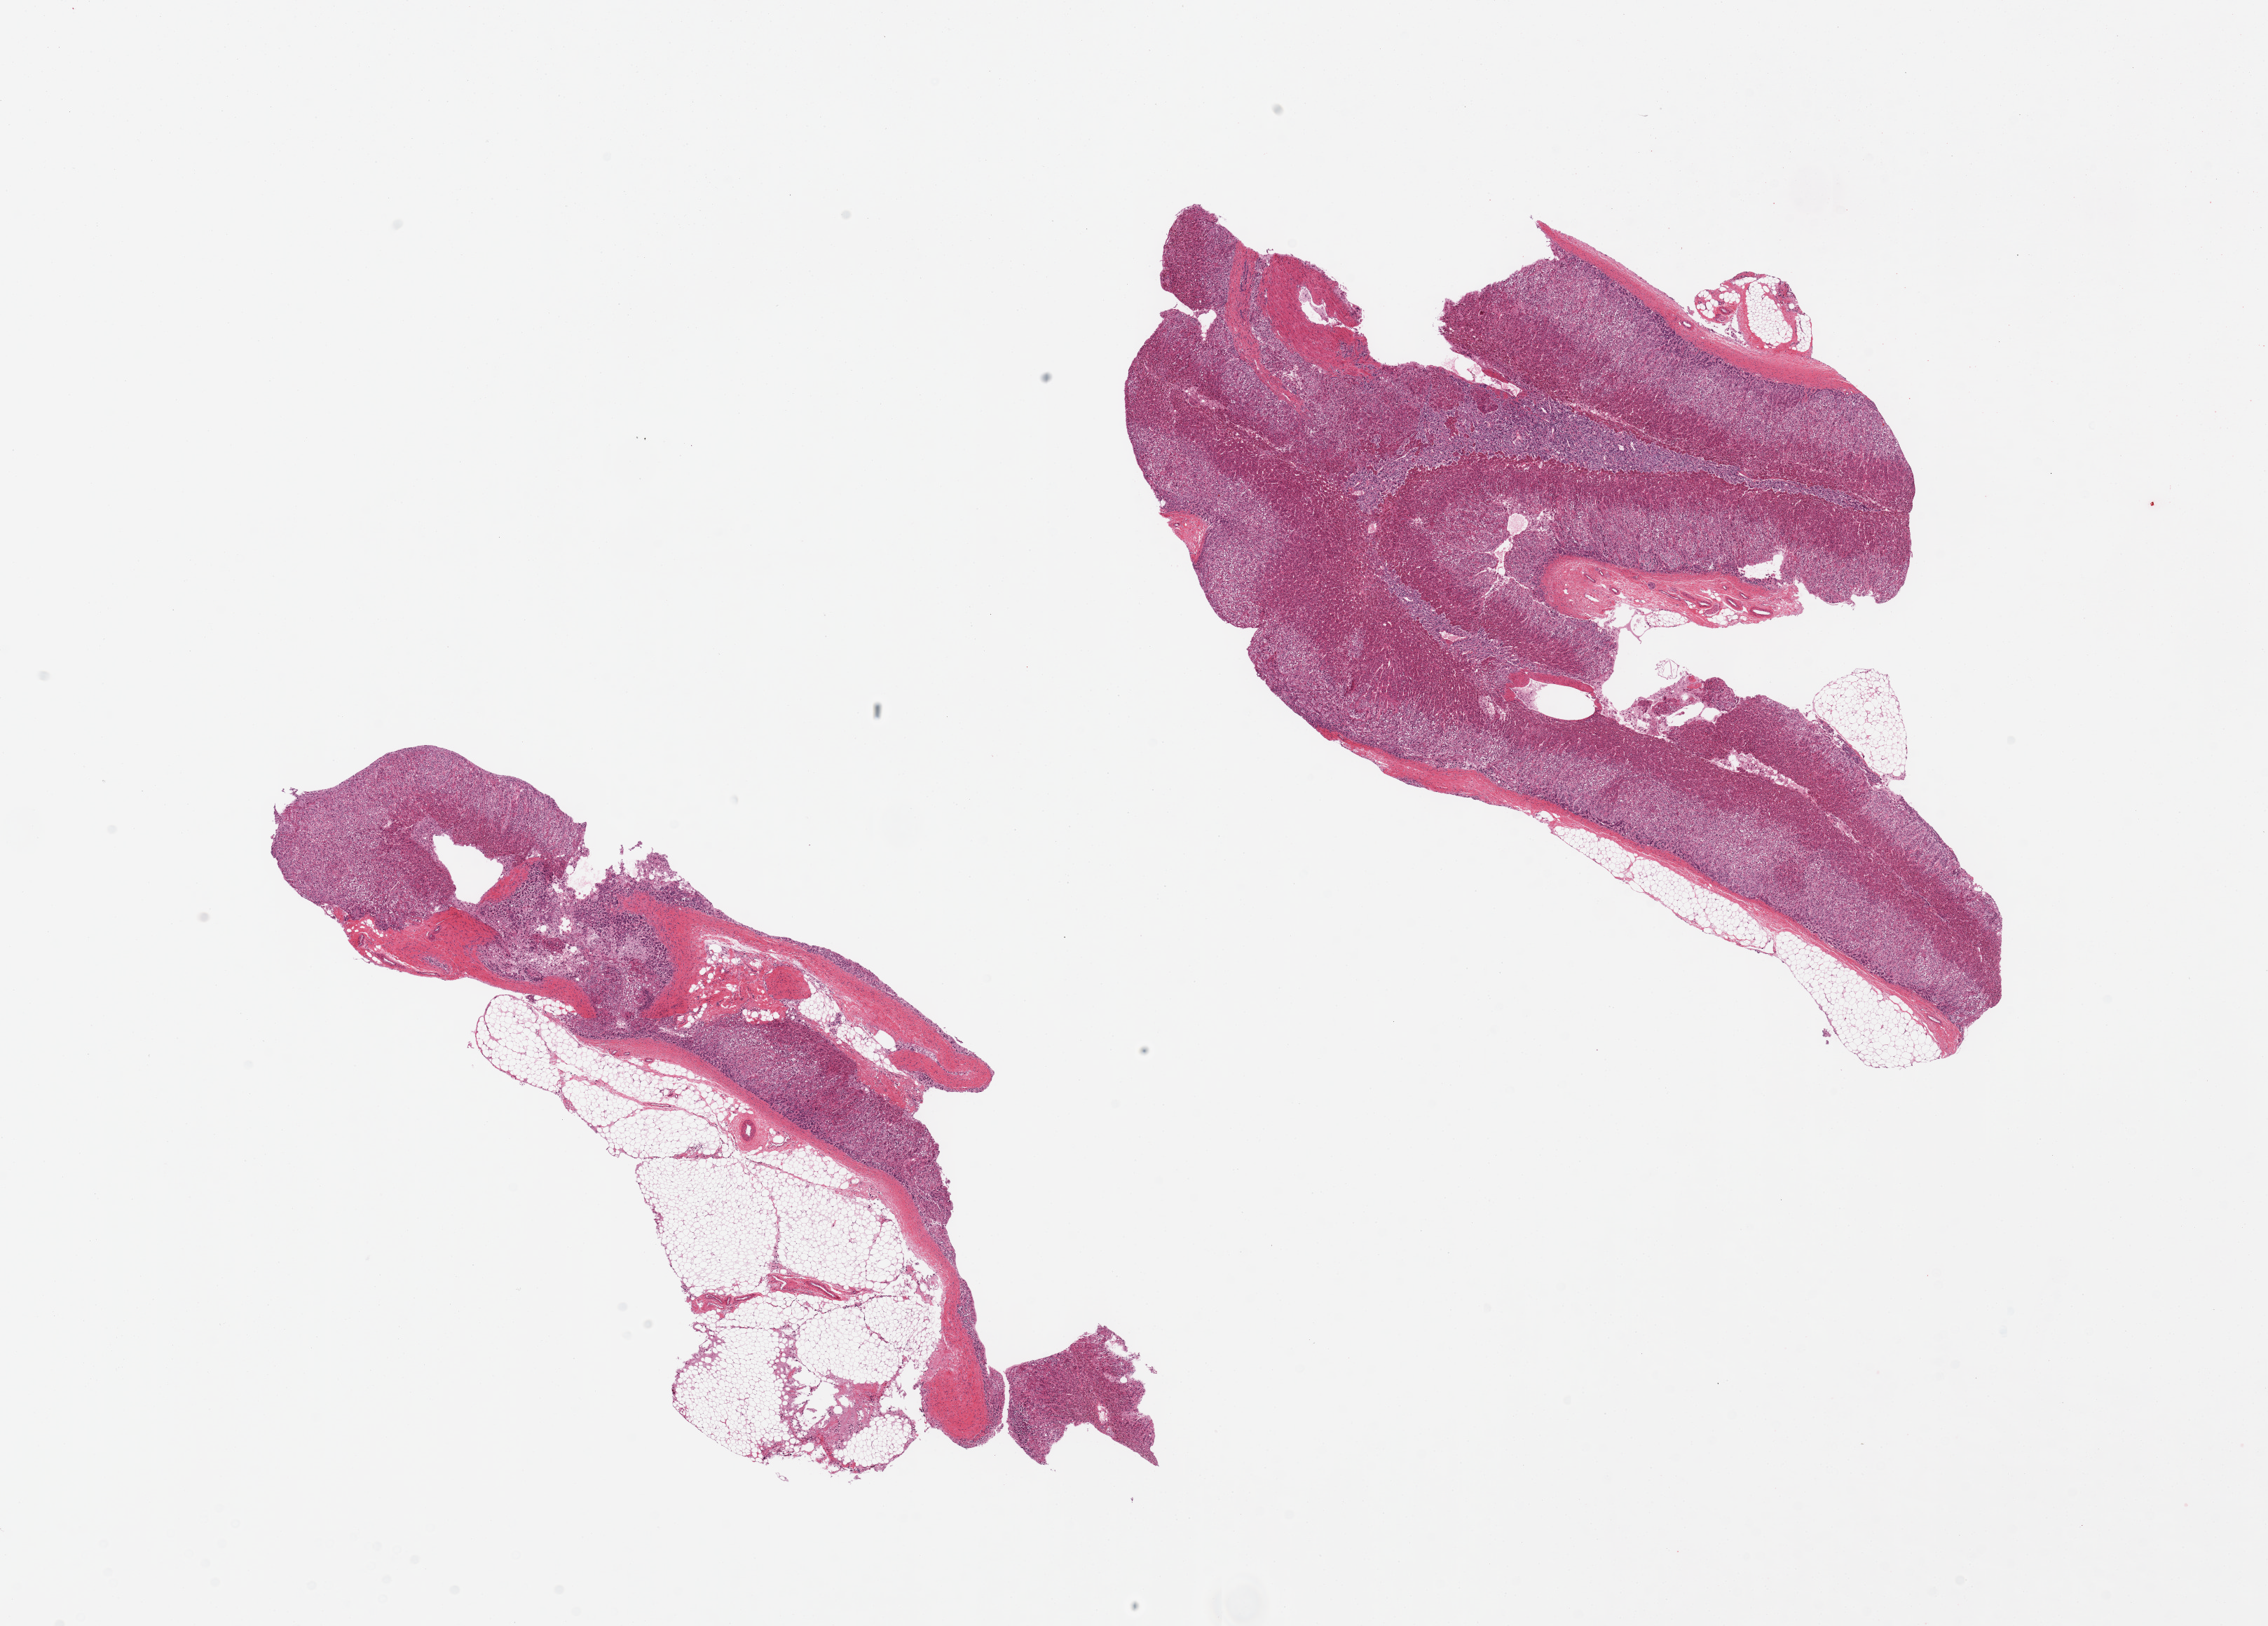
Digitized haematoxylin and eosin-stained section, low-resolution overview of the scanned area, about 25.6 x 18.4 mm, PAXgene-fixed, paraffin-embedded tissue, target tissue: adrenal gland, tissue donor sample. Male donor.
- review note (as recorded): 2 pieces, well preserved; one section shows medulla (delinteated) as well as cortex, the other is cortex and ~40% adherent fat